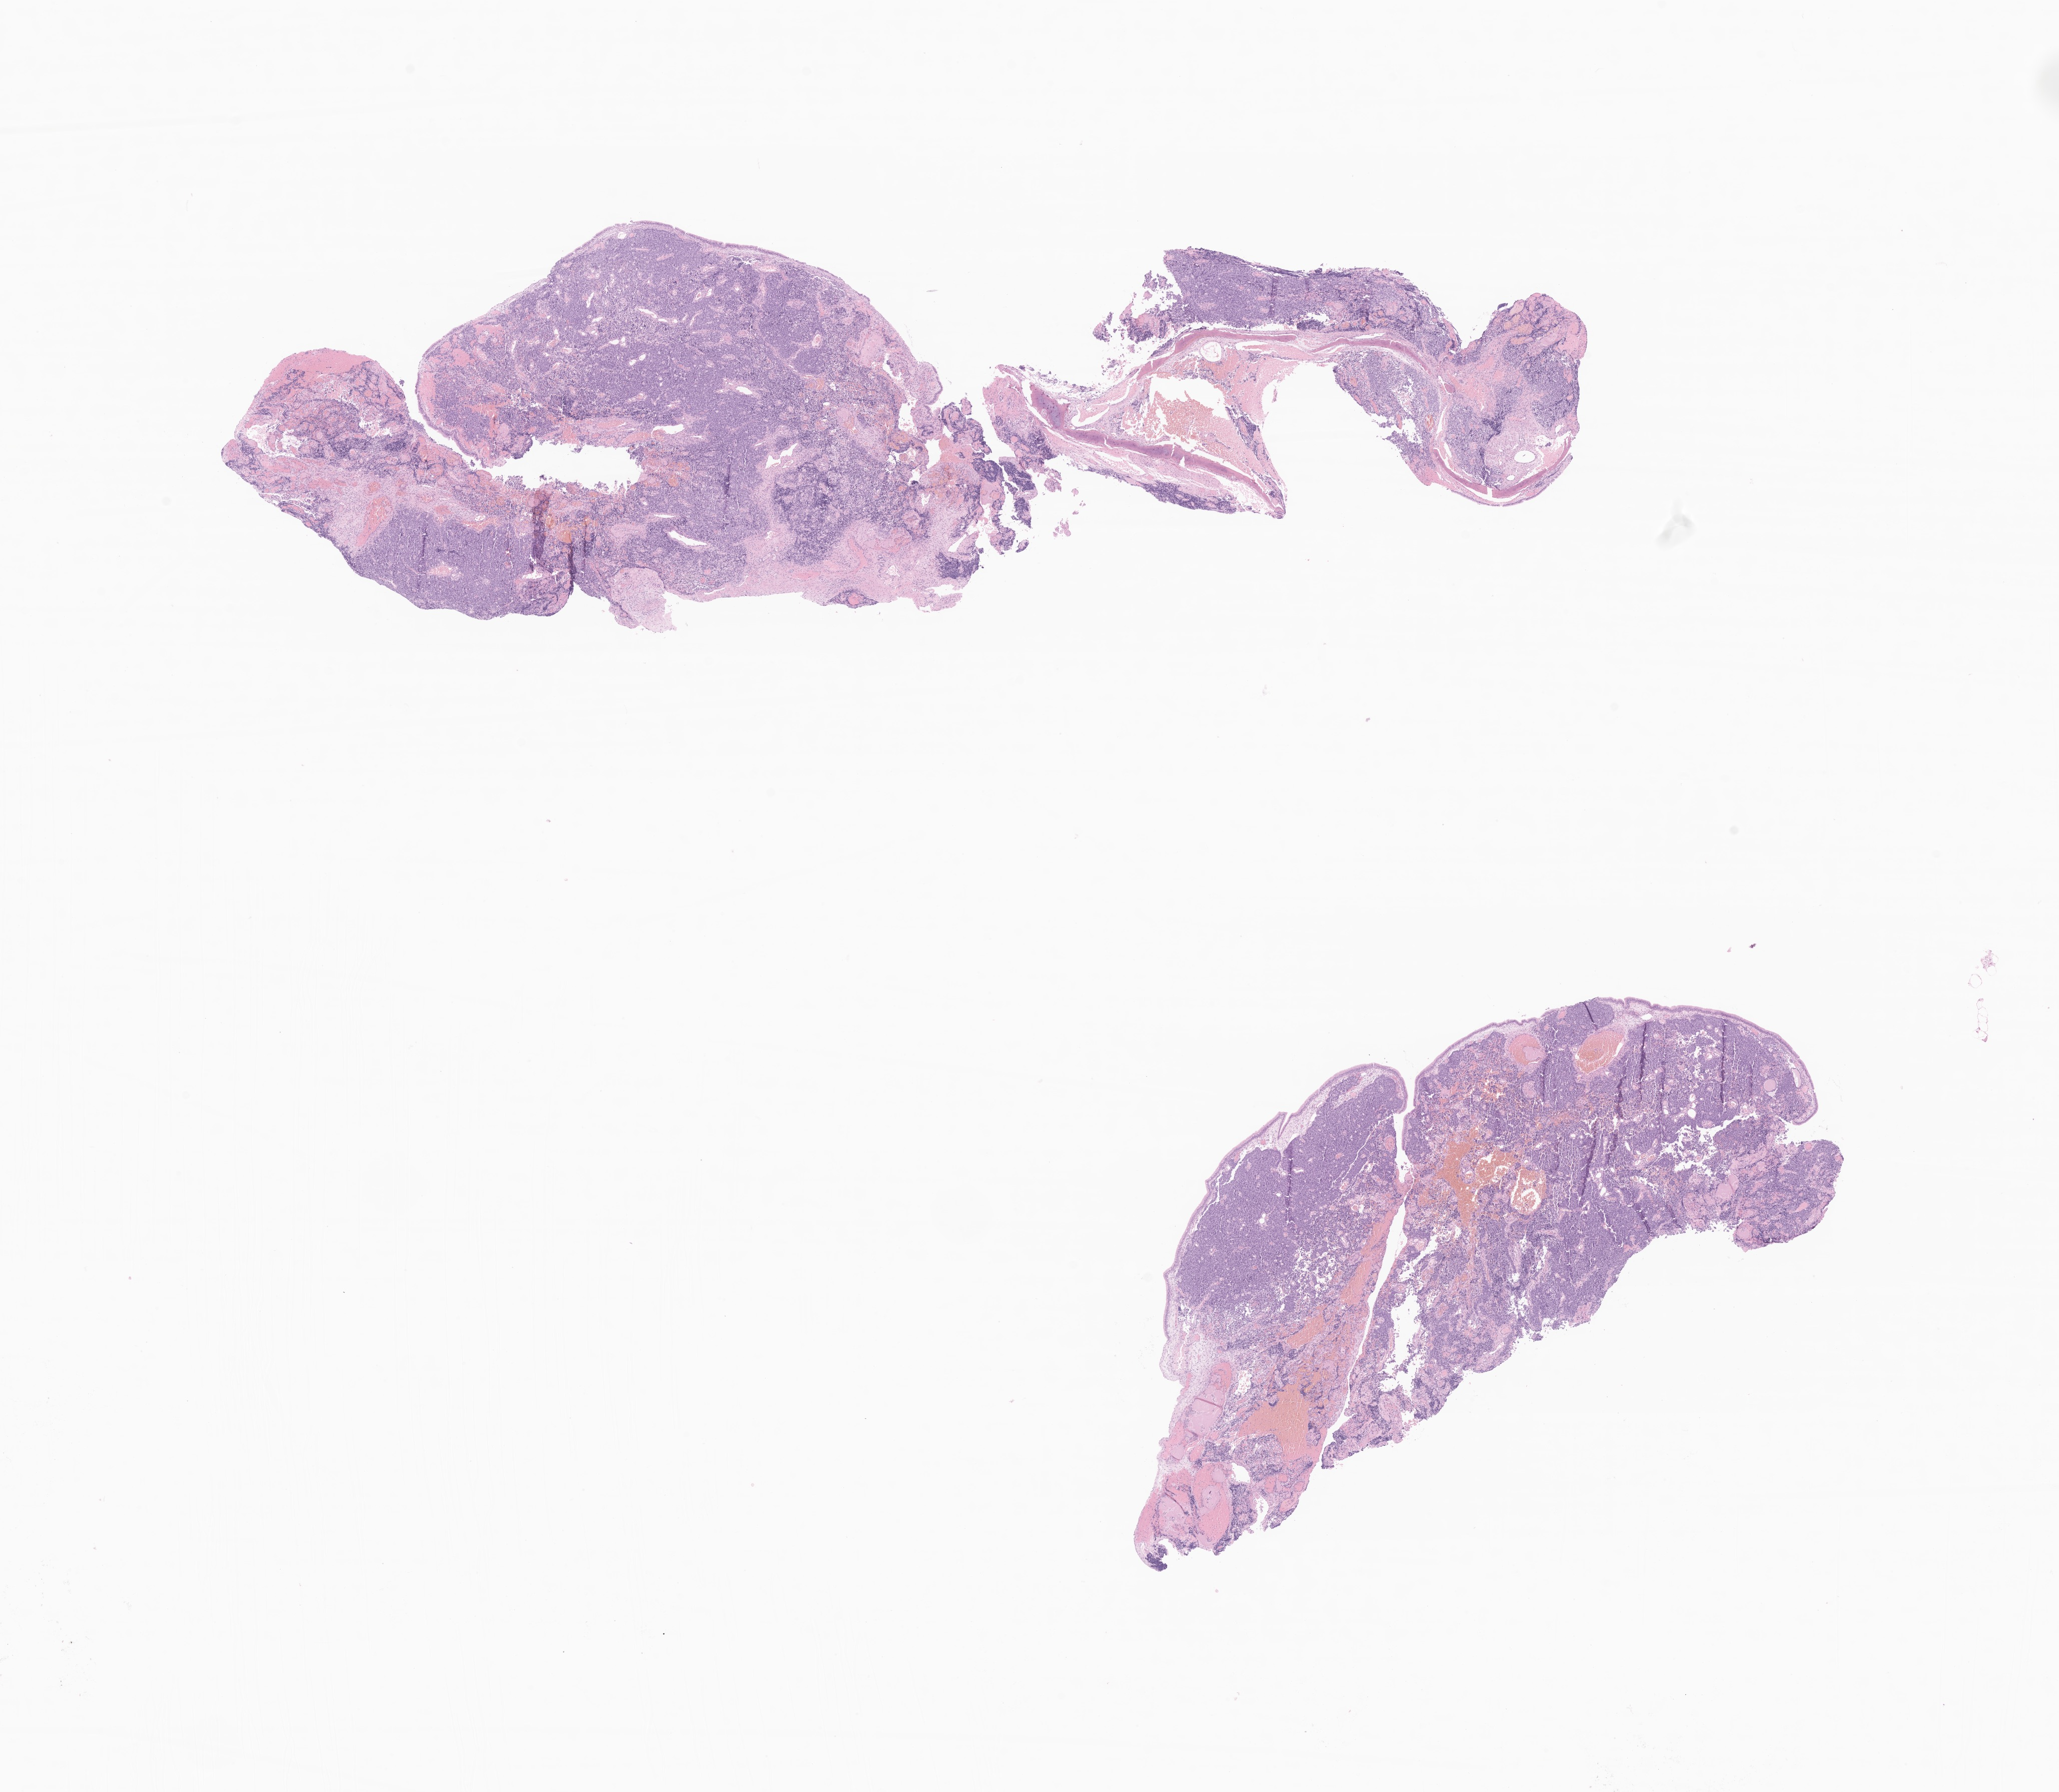
Haematoxylin and eosin whole-slide image of tumor tissue from the nasal cavity, whole scanned area (about 17.4 x 15.1 mm) shown as a low-resolution overview; FFPE section. Patient male; age 204 months.
Recorded diagnosis: Carcinoma, undifferentiated, NOS.